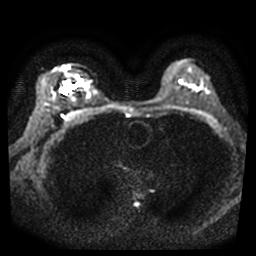
Breast MRI, one axial slice. Position 26 of 40 along the scan axis. Diffusion-weighted series; image 2 of 4 stored at this slice position (different b-values; order by instance number). 3 T. 5 mm slice thickness. 256 × 256 image matrix, field of view 320 × 320 mm. Female patient.
Outlined on this slice (expert manual segmentation):
- tumour on diffusion-weighted imaging: bounding box <65,84,70,92> (left, top, right, bottom; pixels)